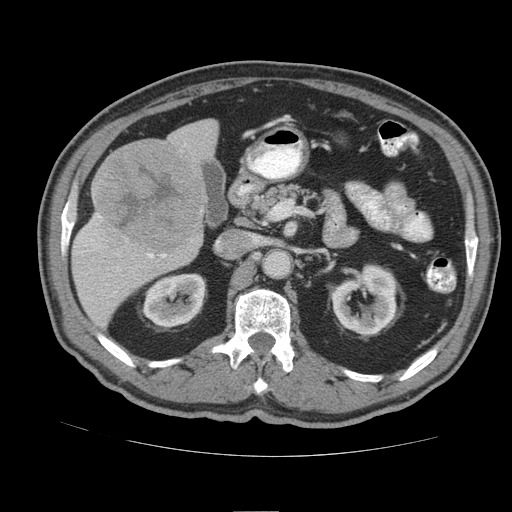
Contrast-enhanced abdominal CT (liver protocol), one axial slice. Slice 43 of 105 in the series (ordered by position). Reconstruction kernel STANDARD. Soft-tissue window (W 400 / L 40 HU). 2.5 mm slice thickness. 512 × 512 image matrix, field of view 380 × 380 mm. Case-level facts recorded for this patient, not image findings: diagnosis: hepatocellular carcinoma (patient treated with transarterial chemoembolisation; whether this scan precedes or follows treatment is not stated here); TNM stage (as recorded): Stage-IIIB; Child-Pugh class: A; tumour nodularity: multinodular.
Annotated regions visible in this slice (semi-automatically segmented with operator editing):
- liver parenchyma outside the tumour (the mass and vessels are separate outlines, so this box may not span the whole liver): bounding box (x1, y1, x2, y2) in pixels: (72, 118, 218, 328)
- mass: (93, 141, 204, 251)
- liver vessels: (83, 214, 166, 293)